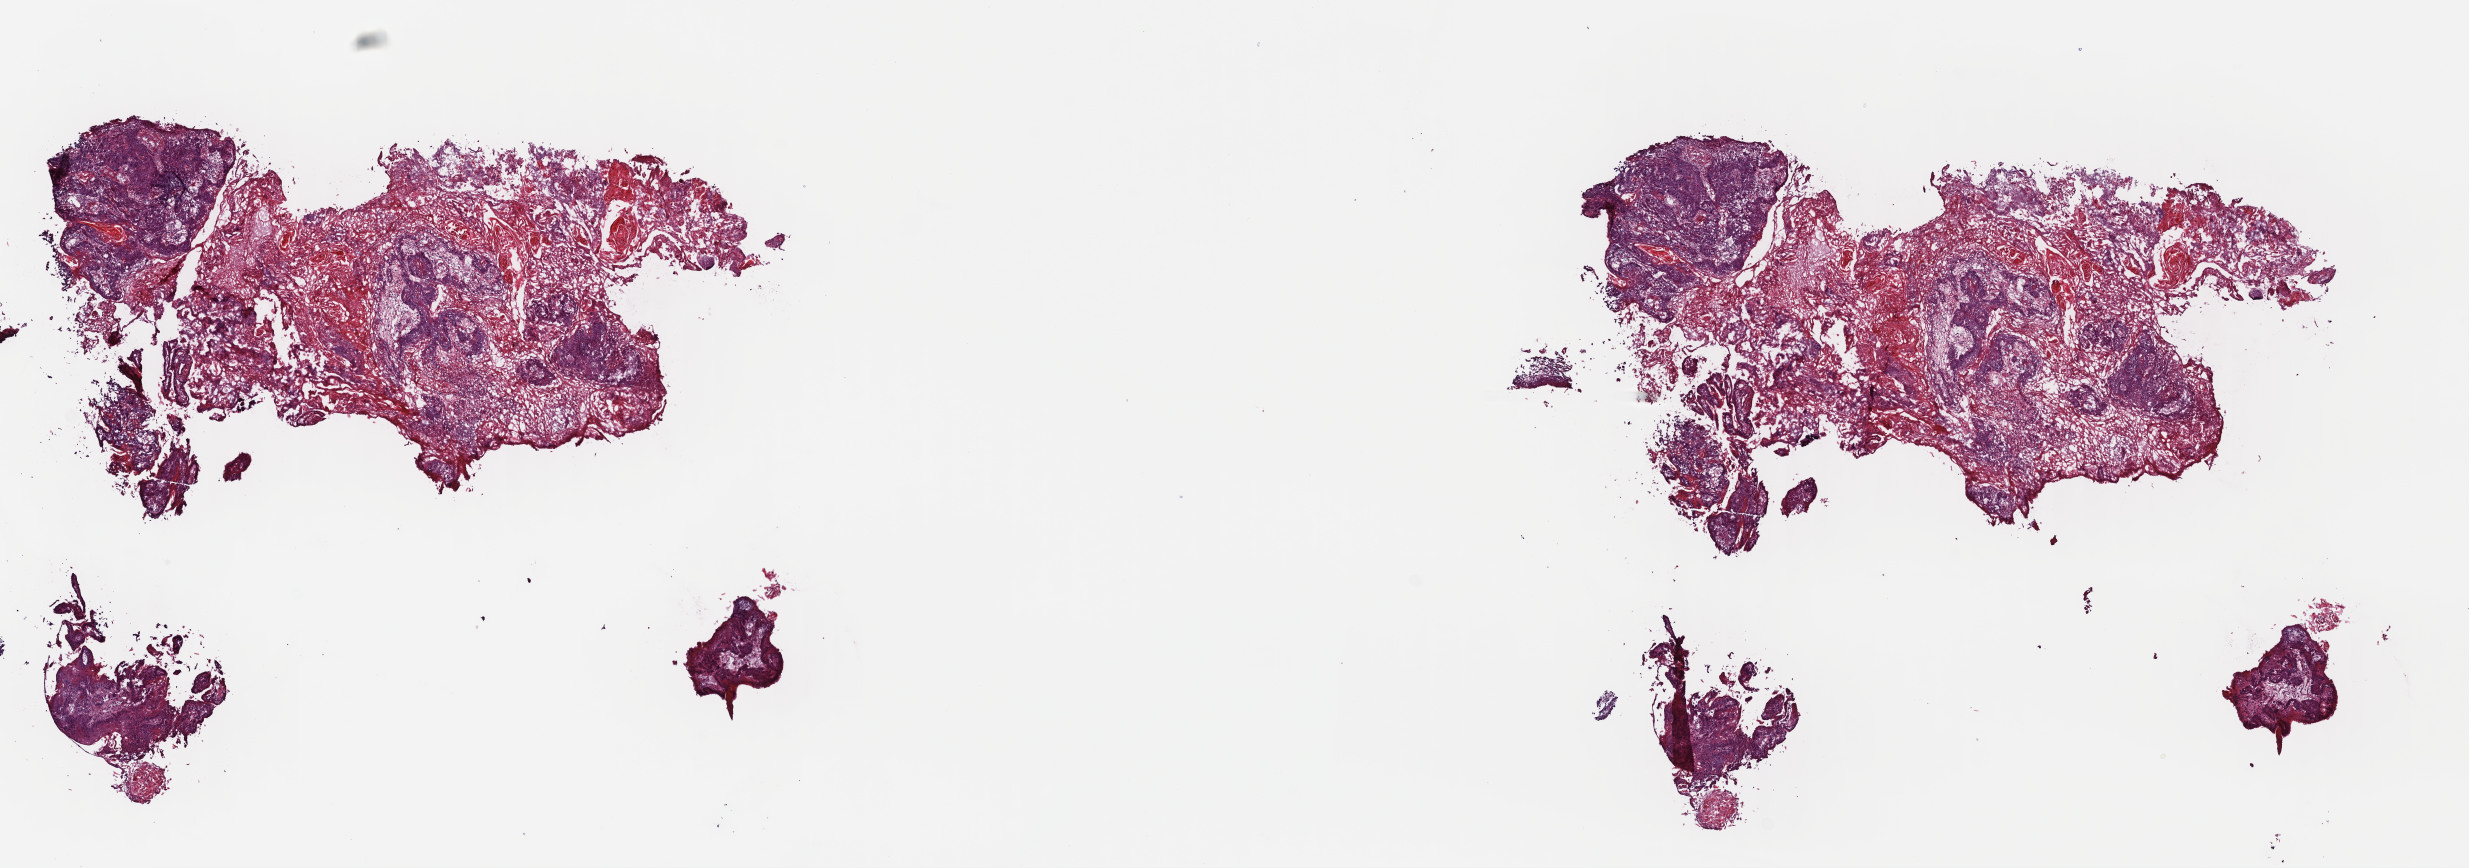
Digitized H&E-stained tissue section (whole slide) — whole scanned area (about 19.4 x 6.8 mm, acquisition: 40x scan) shown as a low-resolution overview. Frozen section from the top of the tissue portion. Sample: primary tumour, head and neck. Male, age 62 years at initial diagnosis. Histologic grade: G2 (moderately differentiated). Pathologist review of this section (percent, as recorded): tumour cells 100%, tumour nuclei 80%, normal cells 0%, stromal cells 0%, necrosis 0%. Infiltration values recorded for this section: lymphocyte infiltration 3%, monocyte infiltration 0%, neutrophil infiltration 1%.
Laterality: left. Histologic diagnosis: Squamous cell carcinoma, keratinizing, NOS (gum, NOS). AJCC pathologic stage: IVA (7th edition). Lymph nodes positive (case pathology): 8 of 101 examined.